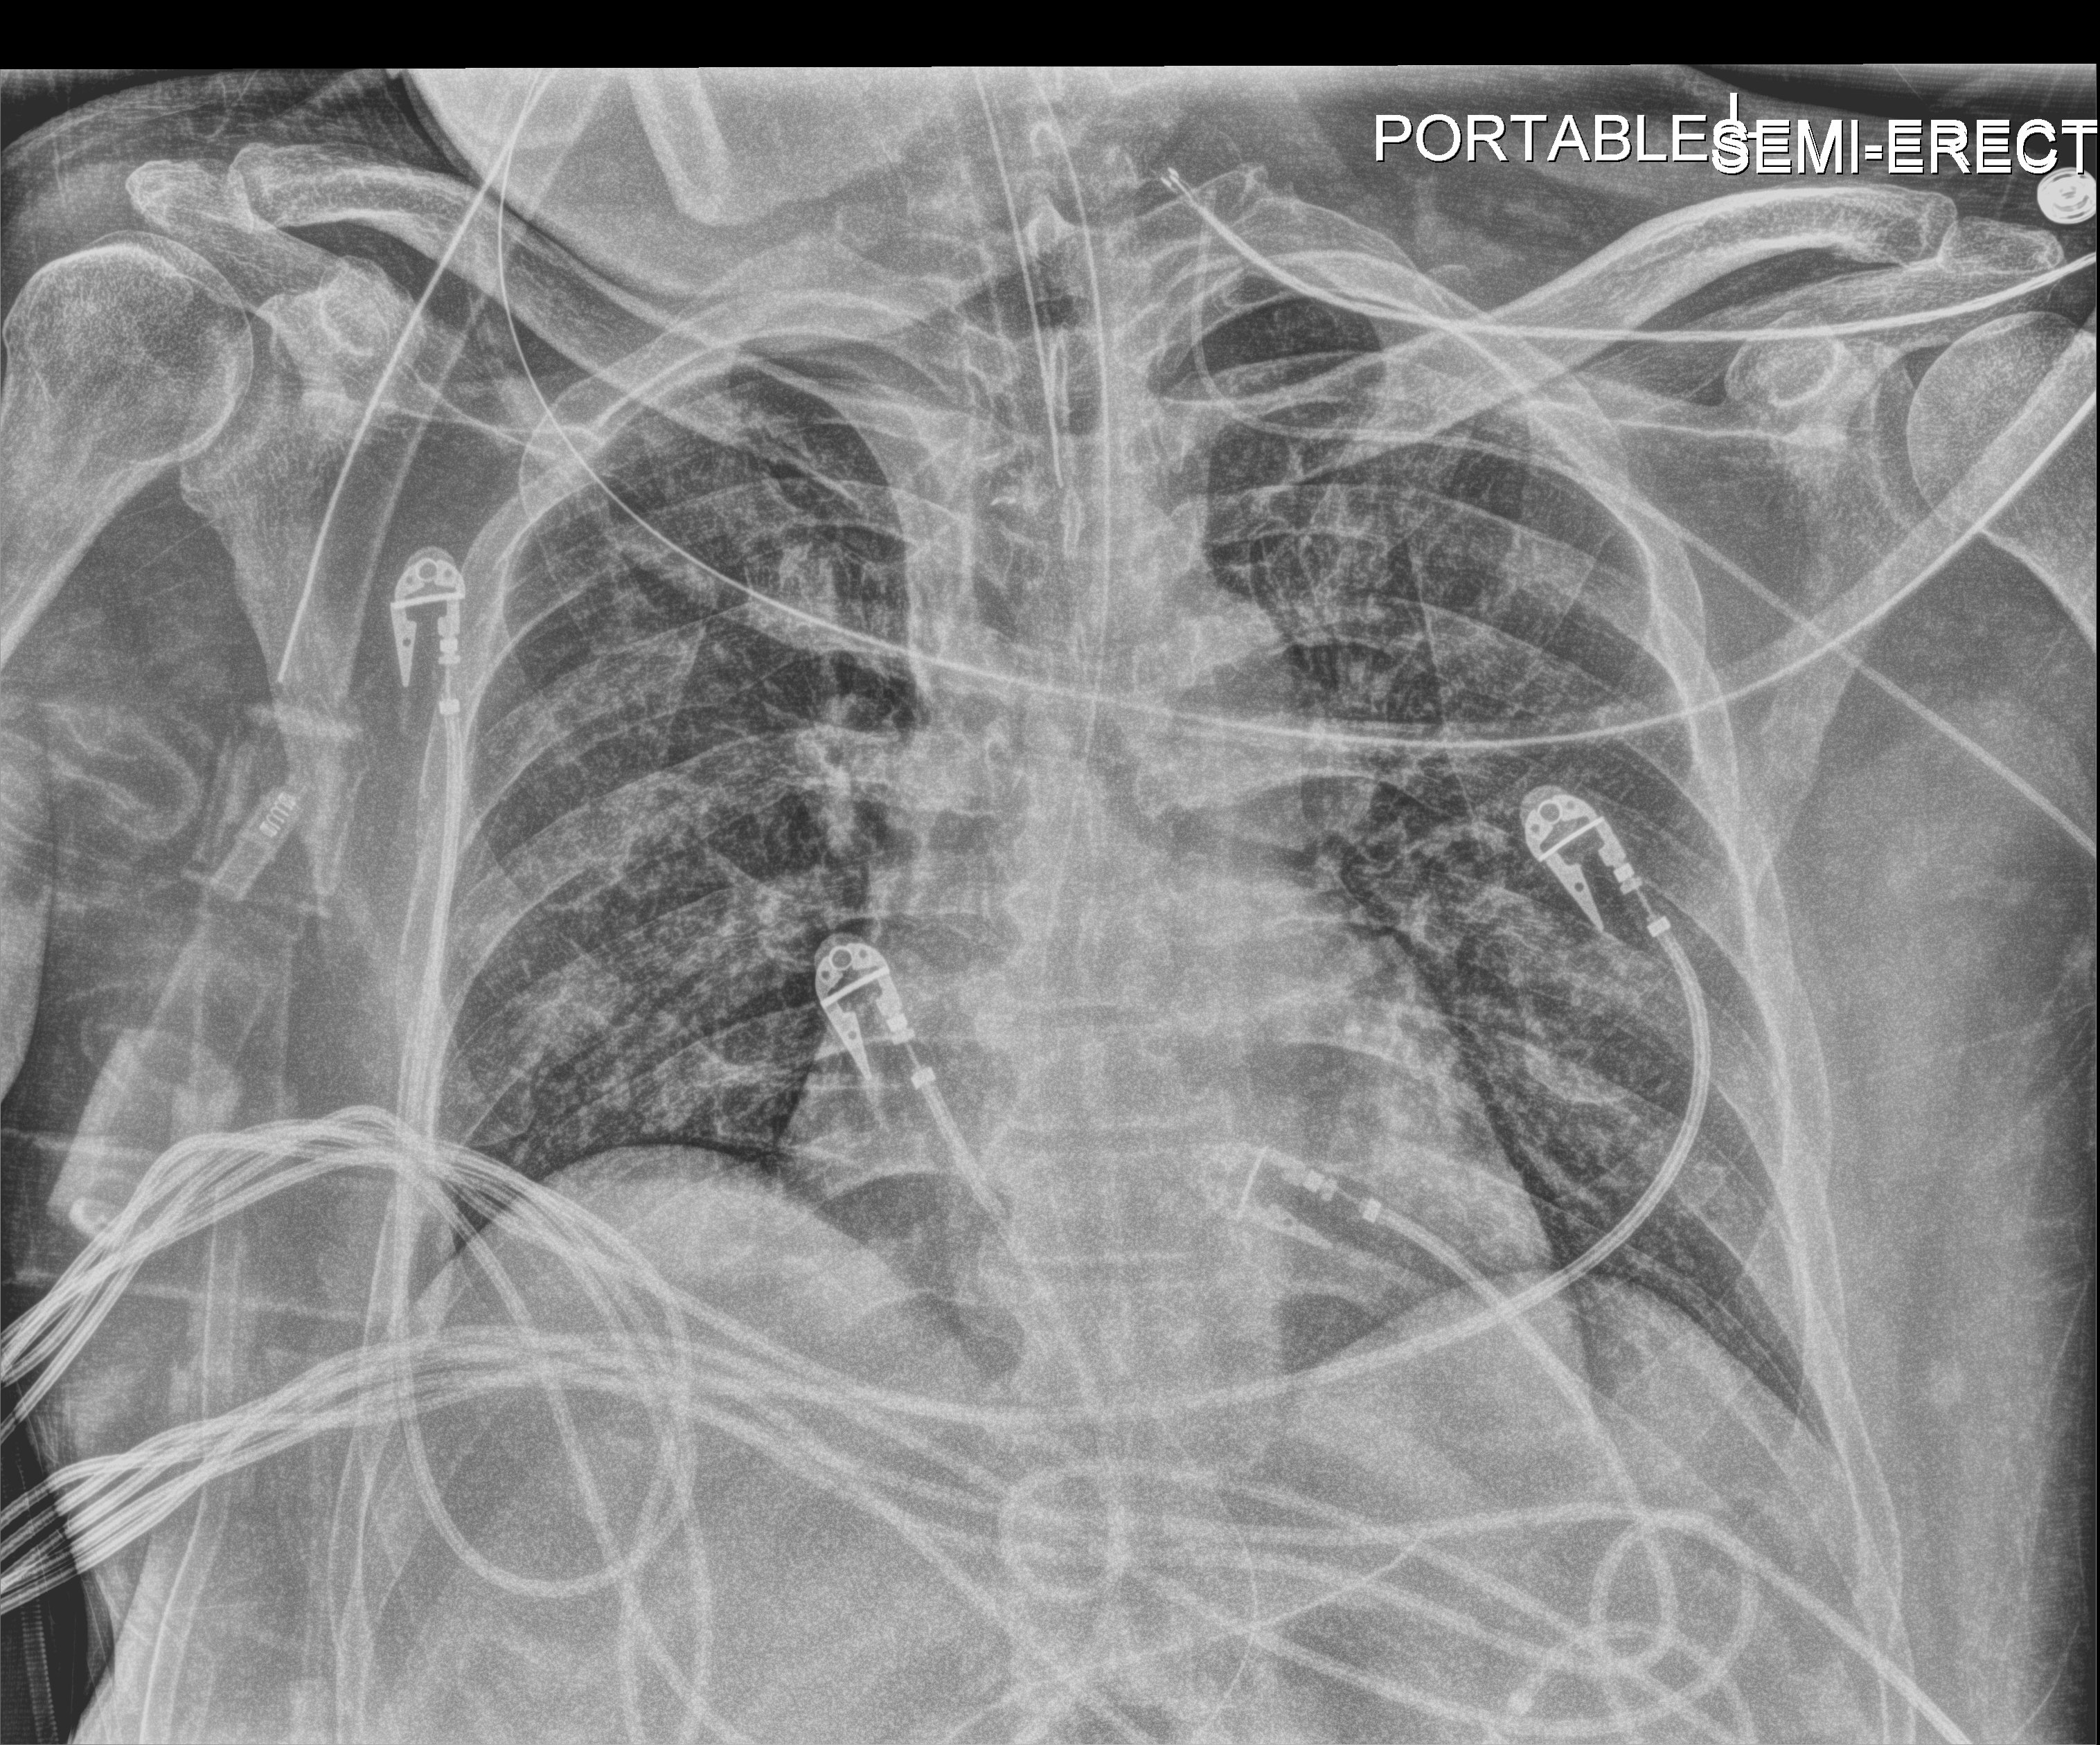
Portable chest radiograph; anteroposterior (AP) projection. Adult patient hospitalised with COVID-19, age 18–59 years.
Hospital-stay facts (about this admission, not read from this image; timing relative to this image not recorded):
- admitted to intensive care during this hospital stay: yes